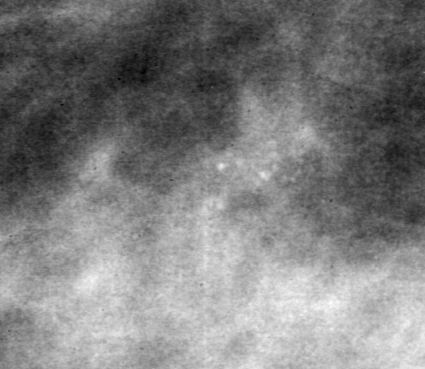
Cropped region of a digitized screen-film mammogram centred on a radiologist-marked abnormality, left breast, MLO view, BI-RADS breast density category 3 (scale 1–4).
Finding: calcifications, morphology pleomorphic, distribution clustered; BI-RADS assessment category 4; subtlety rating 2 on a 1 (subtle) to 5 (obvious) scale; pathology result (as recorded, not read from the image): benign.